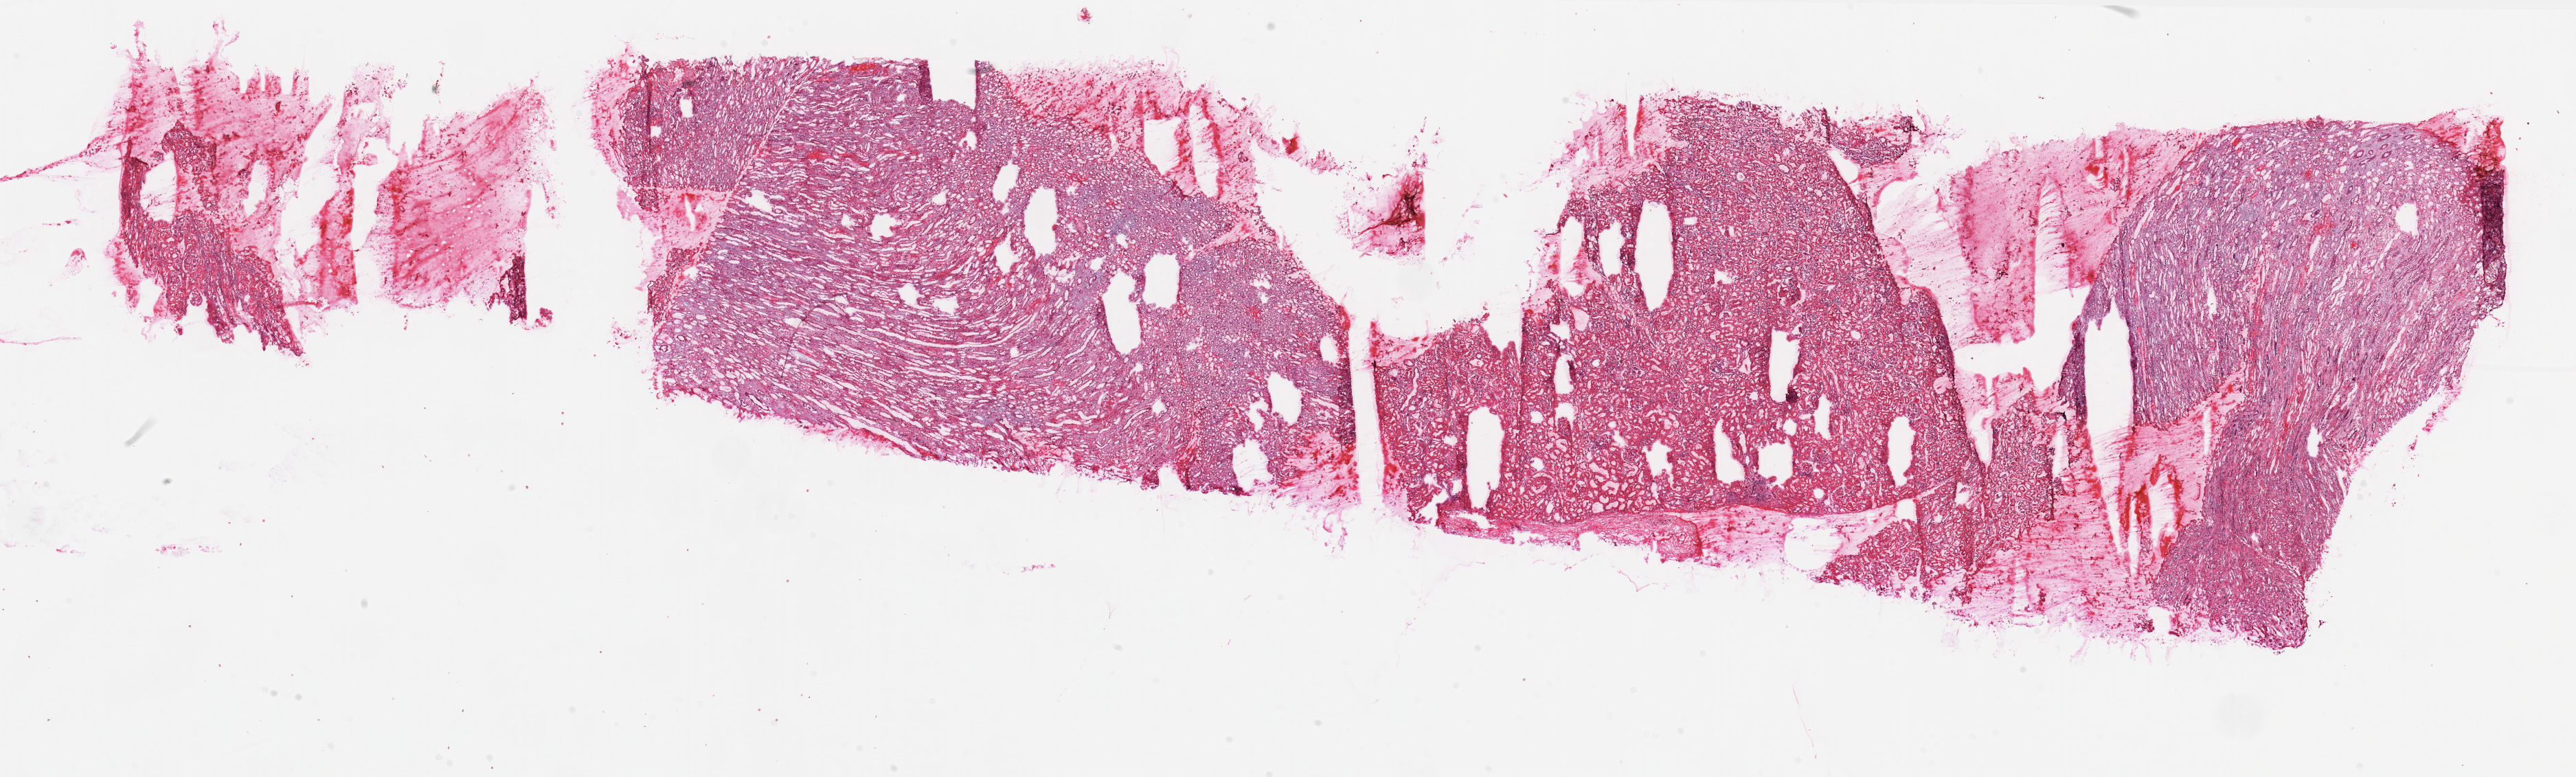
H&E-stained whole-slide image, a low-resolution overview of the entire scanned area, about 30.1 x 9.1 mm. Frozen section from the top of the tissue portion. Kidney, solid tissue normal (non-tumour tissue) sample. Female patient; age at initial diagnosis 58 years.
- this section: solid tissue normal sample (biorepository sample class)
- patient diagnosis: Clear cell adenocarcinoma, NOS